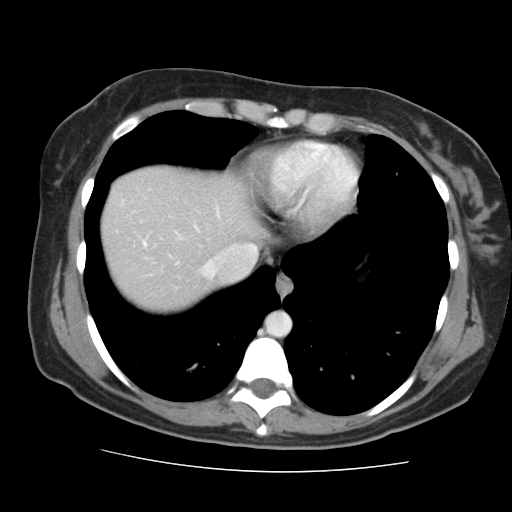
Contrast-enhanced abdominal CT, one axial slice. 120 kVp. Intravenous contrast given. Soft-tissue window (W 400 / L 40 HU). 2.5 mm slice thickness. 512 × 512 image matrix, field of view 333 × 333 mm. Female patient, age 46 years. Case-level facts recorded for this patient, not image findings: diagnosis: colorectal cancer liver metastases, imaged before liver resection; multiple liver metastases: no; largest metastasis: 2.8 cm.
Structures marked on this image (manually delineated by an expert):
- hepatic veins: bounding box <200,244,257,279> (left, top, right, bottom; pixels)
- liver: <102,168,260,310>
- planned liver remnant (the part of the liver to remain after resection): <102,168,260,310>